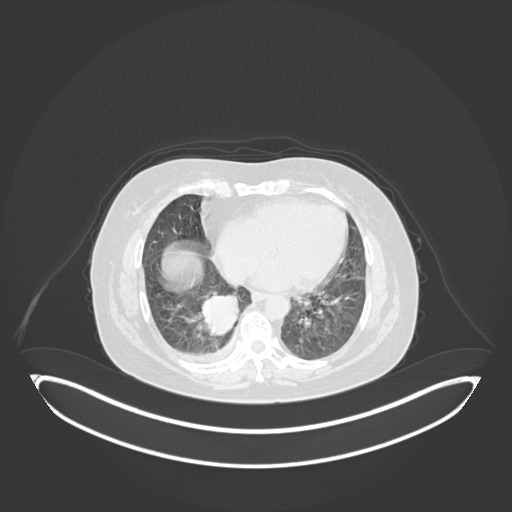
Chest CT, one axial slice. 120 kVp. Lung window (W 1500 / L -600 HU). 1 mm slice thickness. 512 × 512 image matrix, field of view 500 × 500 mm. Female patient, age 56 years. From the clinical record (not read from this slice): clinical TNM (as recorded): T2b N1 M0; histopathological grade: G3.
Outlined on this slice (bounding box drawn by a radiologist):
- lung tumour (recorded histology: small cell carcinoma): bounding box [x1, y1, x2, y2] px = [200, 293, 247, 342]